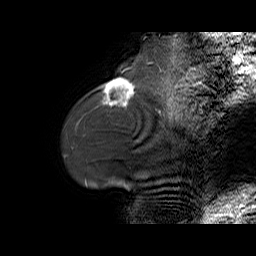
Breast MRI (dynamic contrast-enhanced), one sagittal slice. Position 13 of 70 along the scan axis. Dynamic contrast-enhanced series, time point 2 of 6 at this slice position (early post-contrast). 1.5 T. TE 5.5 ms, TR 32.9 ms. 4 mm slice thickness. 256 × 256 image matrix, field of view 240 × 240 mm. Female patient. From the clinical record (not read from this slice): setting: breast cancer imaged before/during neoadjuvant chemotherapy; receptor status: HER2-positive.
Annotated regions visible in this slice (semi-automatically segmented with operator editing):
- analysis volume of interest (the breast-tissue region the enhancement analysis was run in; not a lesion): bounding box <96,78,141,108> (left, top, right, bottom; pixels)
- tumour enhancement mask (voxels above the 100 % enhancement threshold inside the analysis volume of interest): <103,78,135,106>